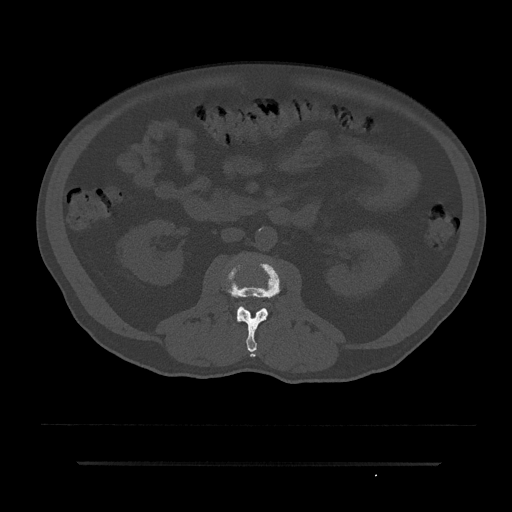
CT including the spine, one axial slice. Slice 51 of 797 in the series (ordered by position). 120 kVp. Bone window (W 1800 / L 400 HU). 0.5 mm slice thickness. 512 × 512 image matrix, field of view 464 × 464 mm. Patient: male, 59 years. From the clinical record (not read from this slice): primary cancer: bile ducts.
Outlined on this slice (semi-automatic segmentation, software-assisted and operator-edited):
- L2 vertebra: bounding box <225,262,282,357> (left, top, right, bottom; pixels)